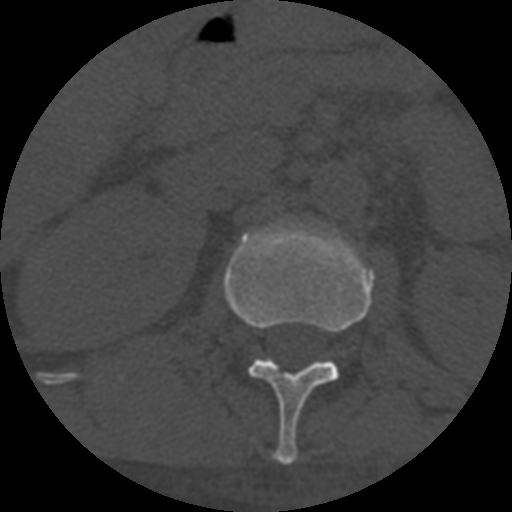
CT including the spine, one axial slice. Slice 281 of 708 in the series (ordered by position). Reconstruction kernel STANDARD. 120 kVp. One of 3 acquisitions stored at this slice position. Bone window (W 1800 / L 400 HU). 1.25 mm slice thickness. 512 × 512 image matrix. Patient age 55 years. Case-level facts recorded for this patient, not image findings: primary cancer: colon.
Structures marked on this image (semi-automatically segmented with operator editing):
- L1 vertebra: bounding box [x1, y1, x2, y2] px = [224, 221, 375, 465]